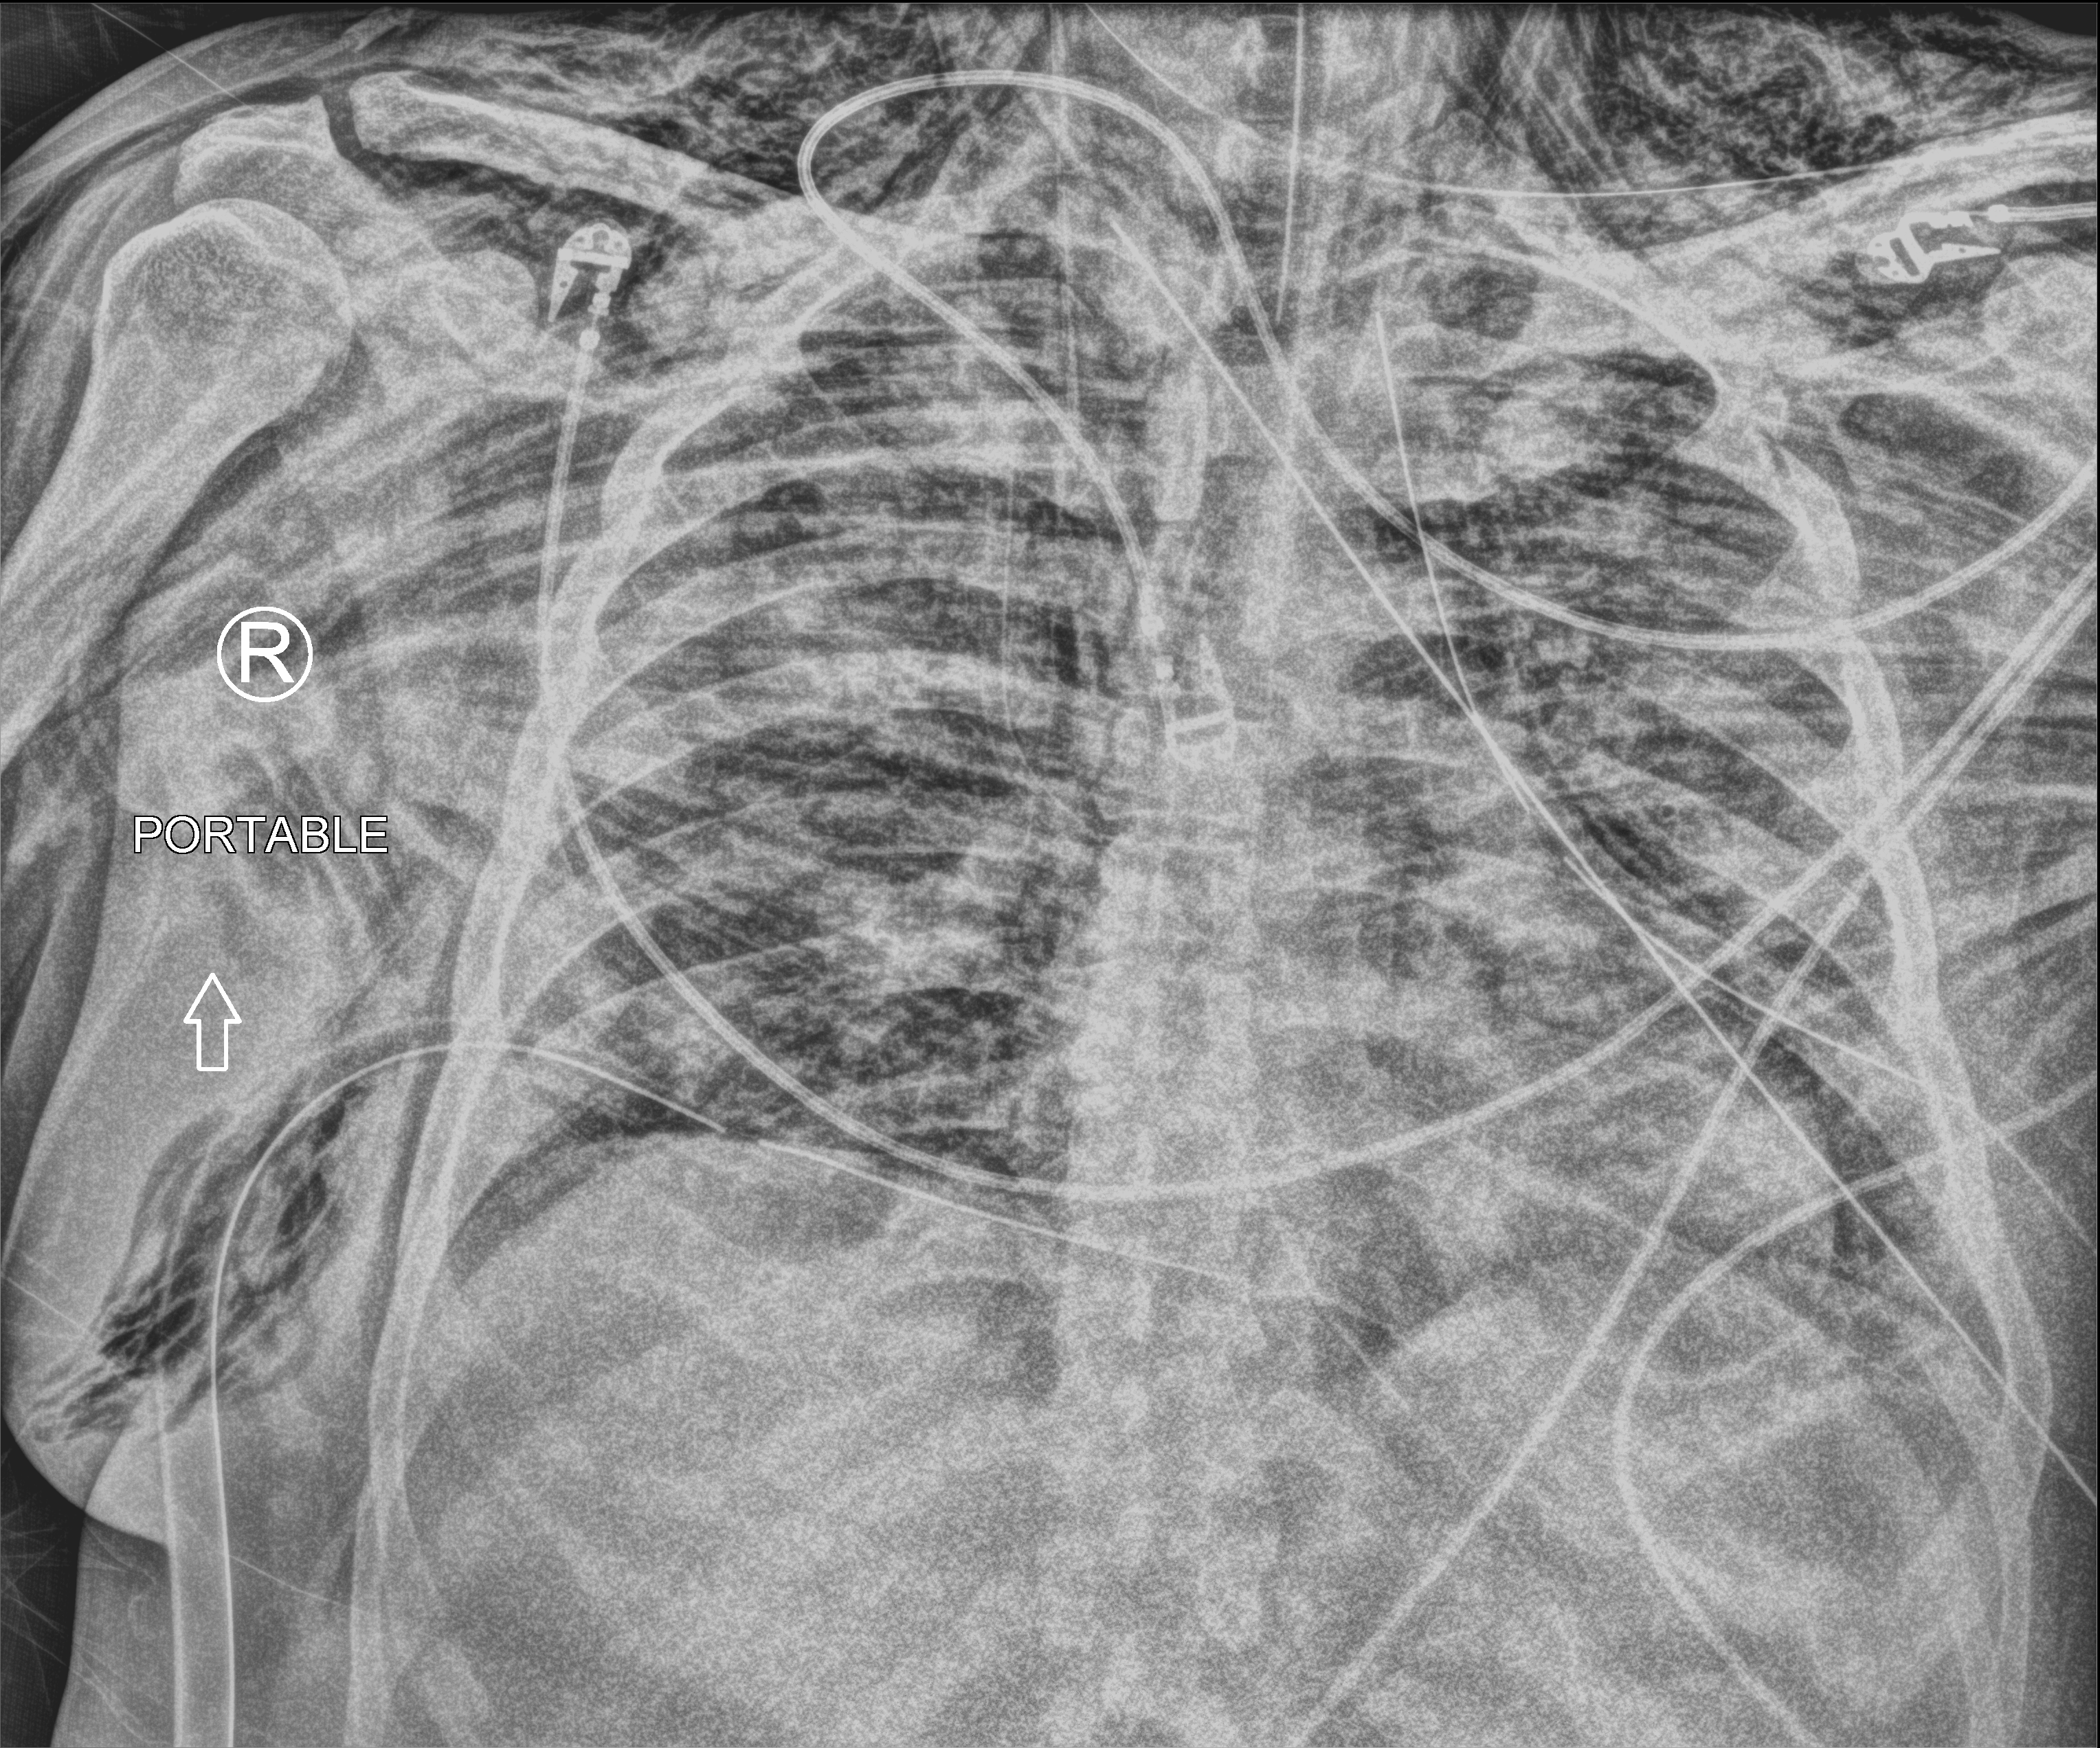
Portable chest radiograph, anteroposterior (AP) projection. Patient hospitalised with COVID-19; male, aged 18–59 years.
Admission-level facts for this patient (not findings on this image; timing relative to this image not recorded):
- admitted to intensive care during this hospital stay: yes
- mechanically ventilated during this hospital stay: yes
- length of hospital stay: 29 days